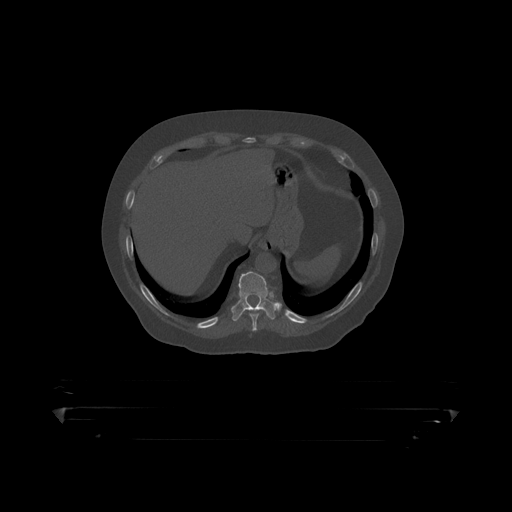
CT including the spine, one axial slice; slice 221 of 390 in the series (ordered by position); bone window (W 1800 / L 400 HU); 512 × 512 image matrix. Male patient, age 60 years. Case-level facts recorded for this patient, not image findings: primary cancer: prostate.
Annotated regions visible in this slice (semi-automatically segmented with operator editing):
- T10 vertebra: bounding box [x1, y1, x2, y2] px = [232, 272, 278, 318]
- T9 vertebra: [250, 310, 259, 319]